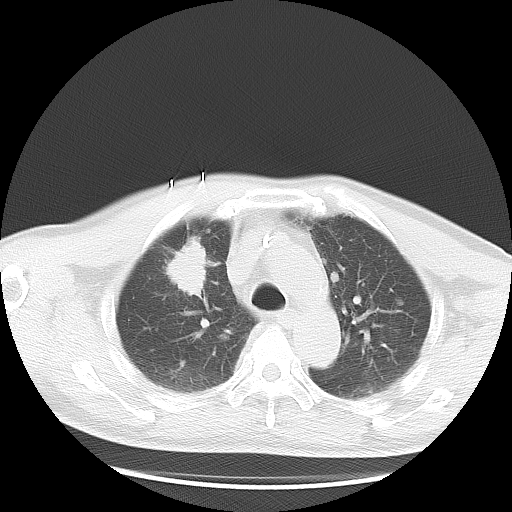
Chest CT, one axial slice. Slice 22 of 36 in the series (ordered by position). 120 kVp. Lung window (W 1500 / L -600 HU). 512 × 512 image matrix. Male patient, age 57 years. From the clinical record (not read from this slice): clinical TNM (as recorded): T2 N3 M1a.
Annotated regions visible in this slice (rectangle marked by the reading radiologist):
- lung tumour (recorded histology: adenocarcinoma): bounding box (x1, y1, x2, y2) in pixels: (160, 236, 210, 303)